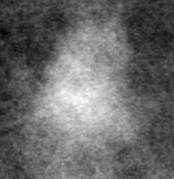
Crop from a digitized film mammogram around one marked abnormality; left breast; CC view.
Marked abnormality: mass, shape irregular, margins obscured; BI-RADS assessment category 0; pathology result (as recorded, not read from the image): benign.